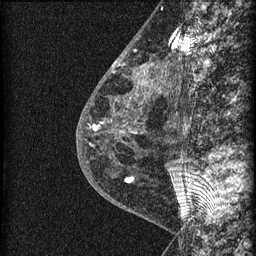
Breast MRI (dynamic contrast-enhanced), one sagittal slice; position 22 of 60 along the scan axis; dynamic contrast-enhanced series, image 2 of 3 at this slice position (ordered by acquisition); 1.5 T; TE 4.2 ms, TR 22.7 ms; 256 × 256 image matrix, field of view 180 × 180 mm. Patient: female, 48 years. From the clinical record (not read from this slice): setting: breast cancer imaged before/during neoadjuvant chemotherapy; receptor status: triple-negative.
Annotated regions visible in this slice (semi-automatically segmented with operator editing):
- analysis volume of interest (the breast-tissue region the enhancement analysis was run in; not a lesion): bounding box <115,34,169,162> (left, top, right, bottom; pixels)
- tumour enhancement mask (voxels above the 90 % enhancement threshold inside the analysis volume of interest): <142,69,145,73>